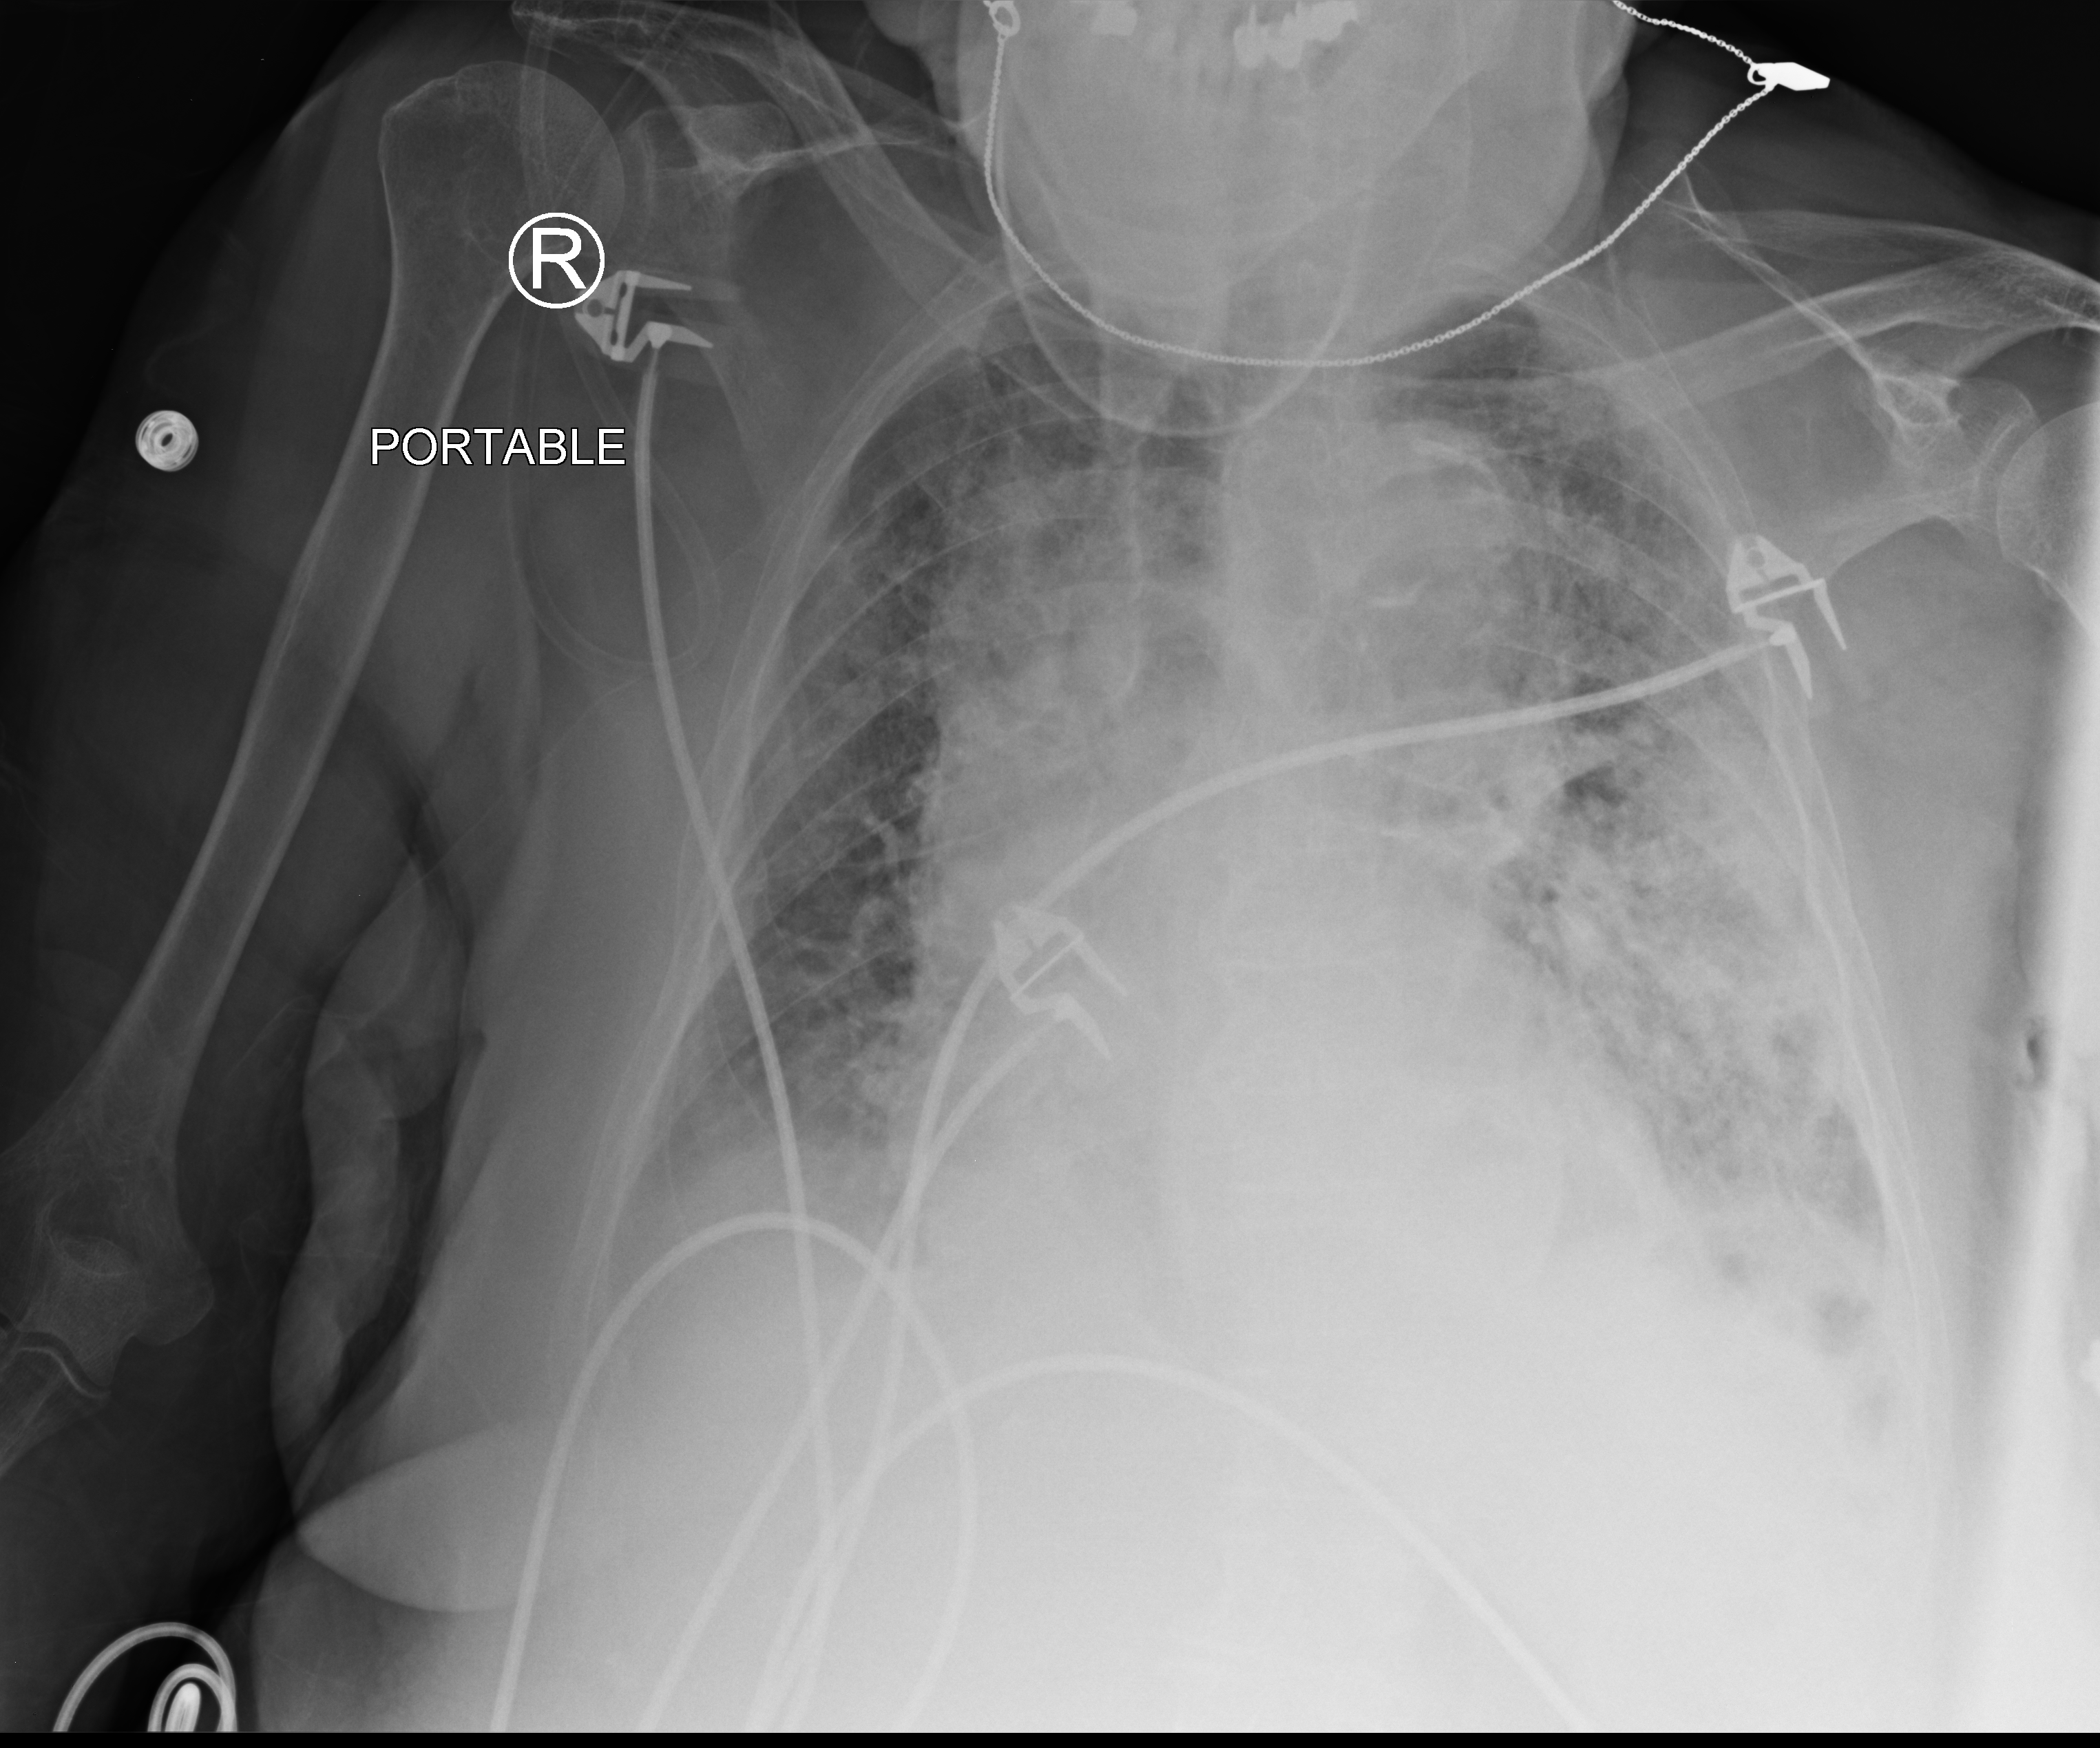
Portable chest radiograph, anteroposterior (AP) projection. Female patient hospitalised with COVID-19, age 75–90 years.
Hospital-stay facts (about this admission, not read from this image; timing relative to this image not recorded): other chronic lung disease (admission record): no; mechanically ventilated during this hospital stay: no; length of hospital stay: 13 days.